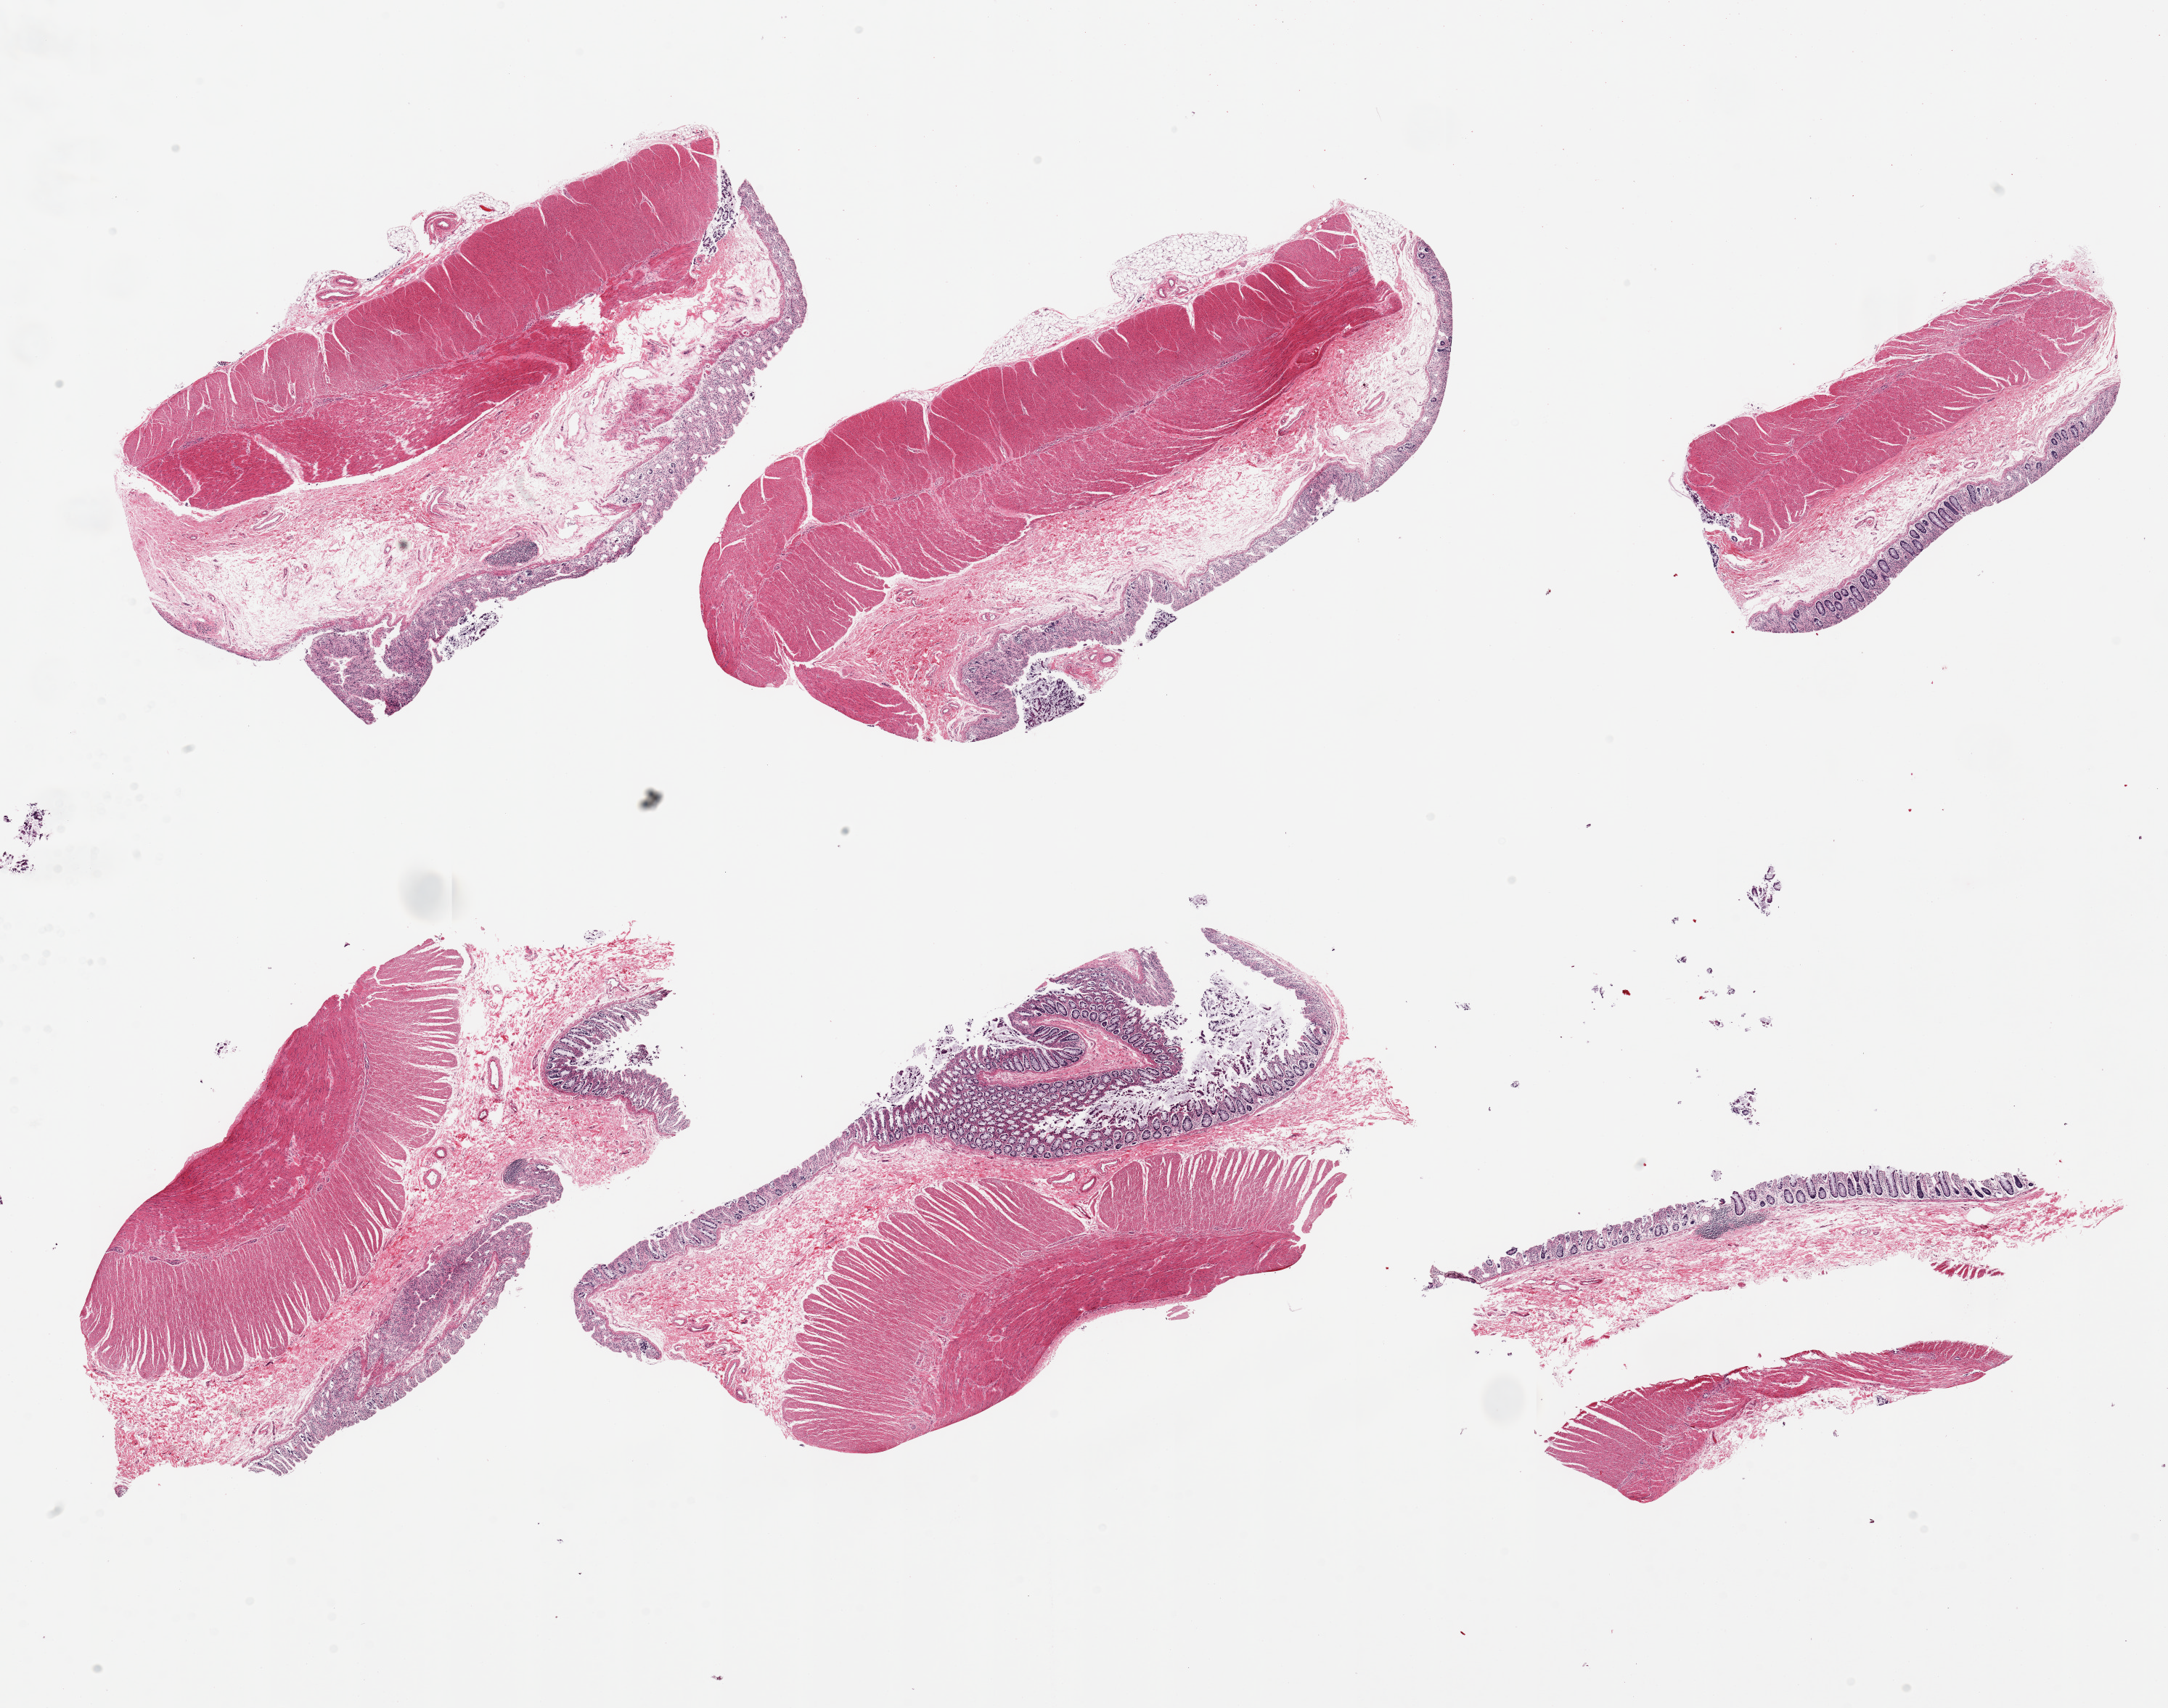
Haematoxylin and eosin whole-slide image — shown as a low-resolution overview of the whole scanned area (about 23.6 x 18.6 mm, slide scanned at 20x). Donor sex: male.
* specimen: PAXgene-fixed, paraffin-embedded tissue; sampled site (target tissue): sigmoid colon; tissue donor sample